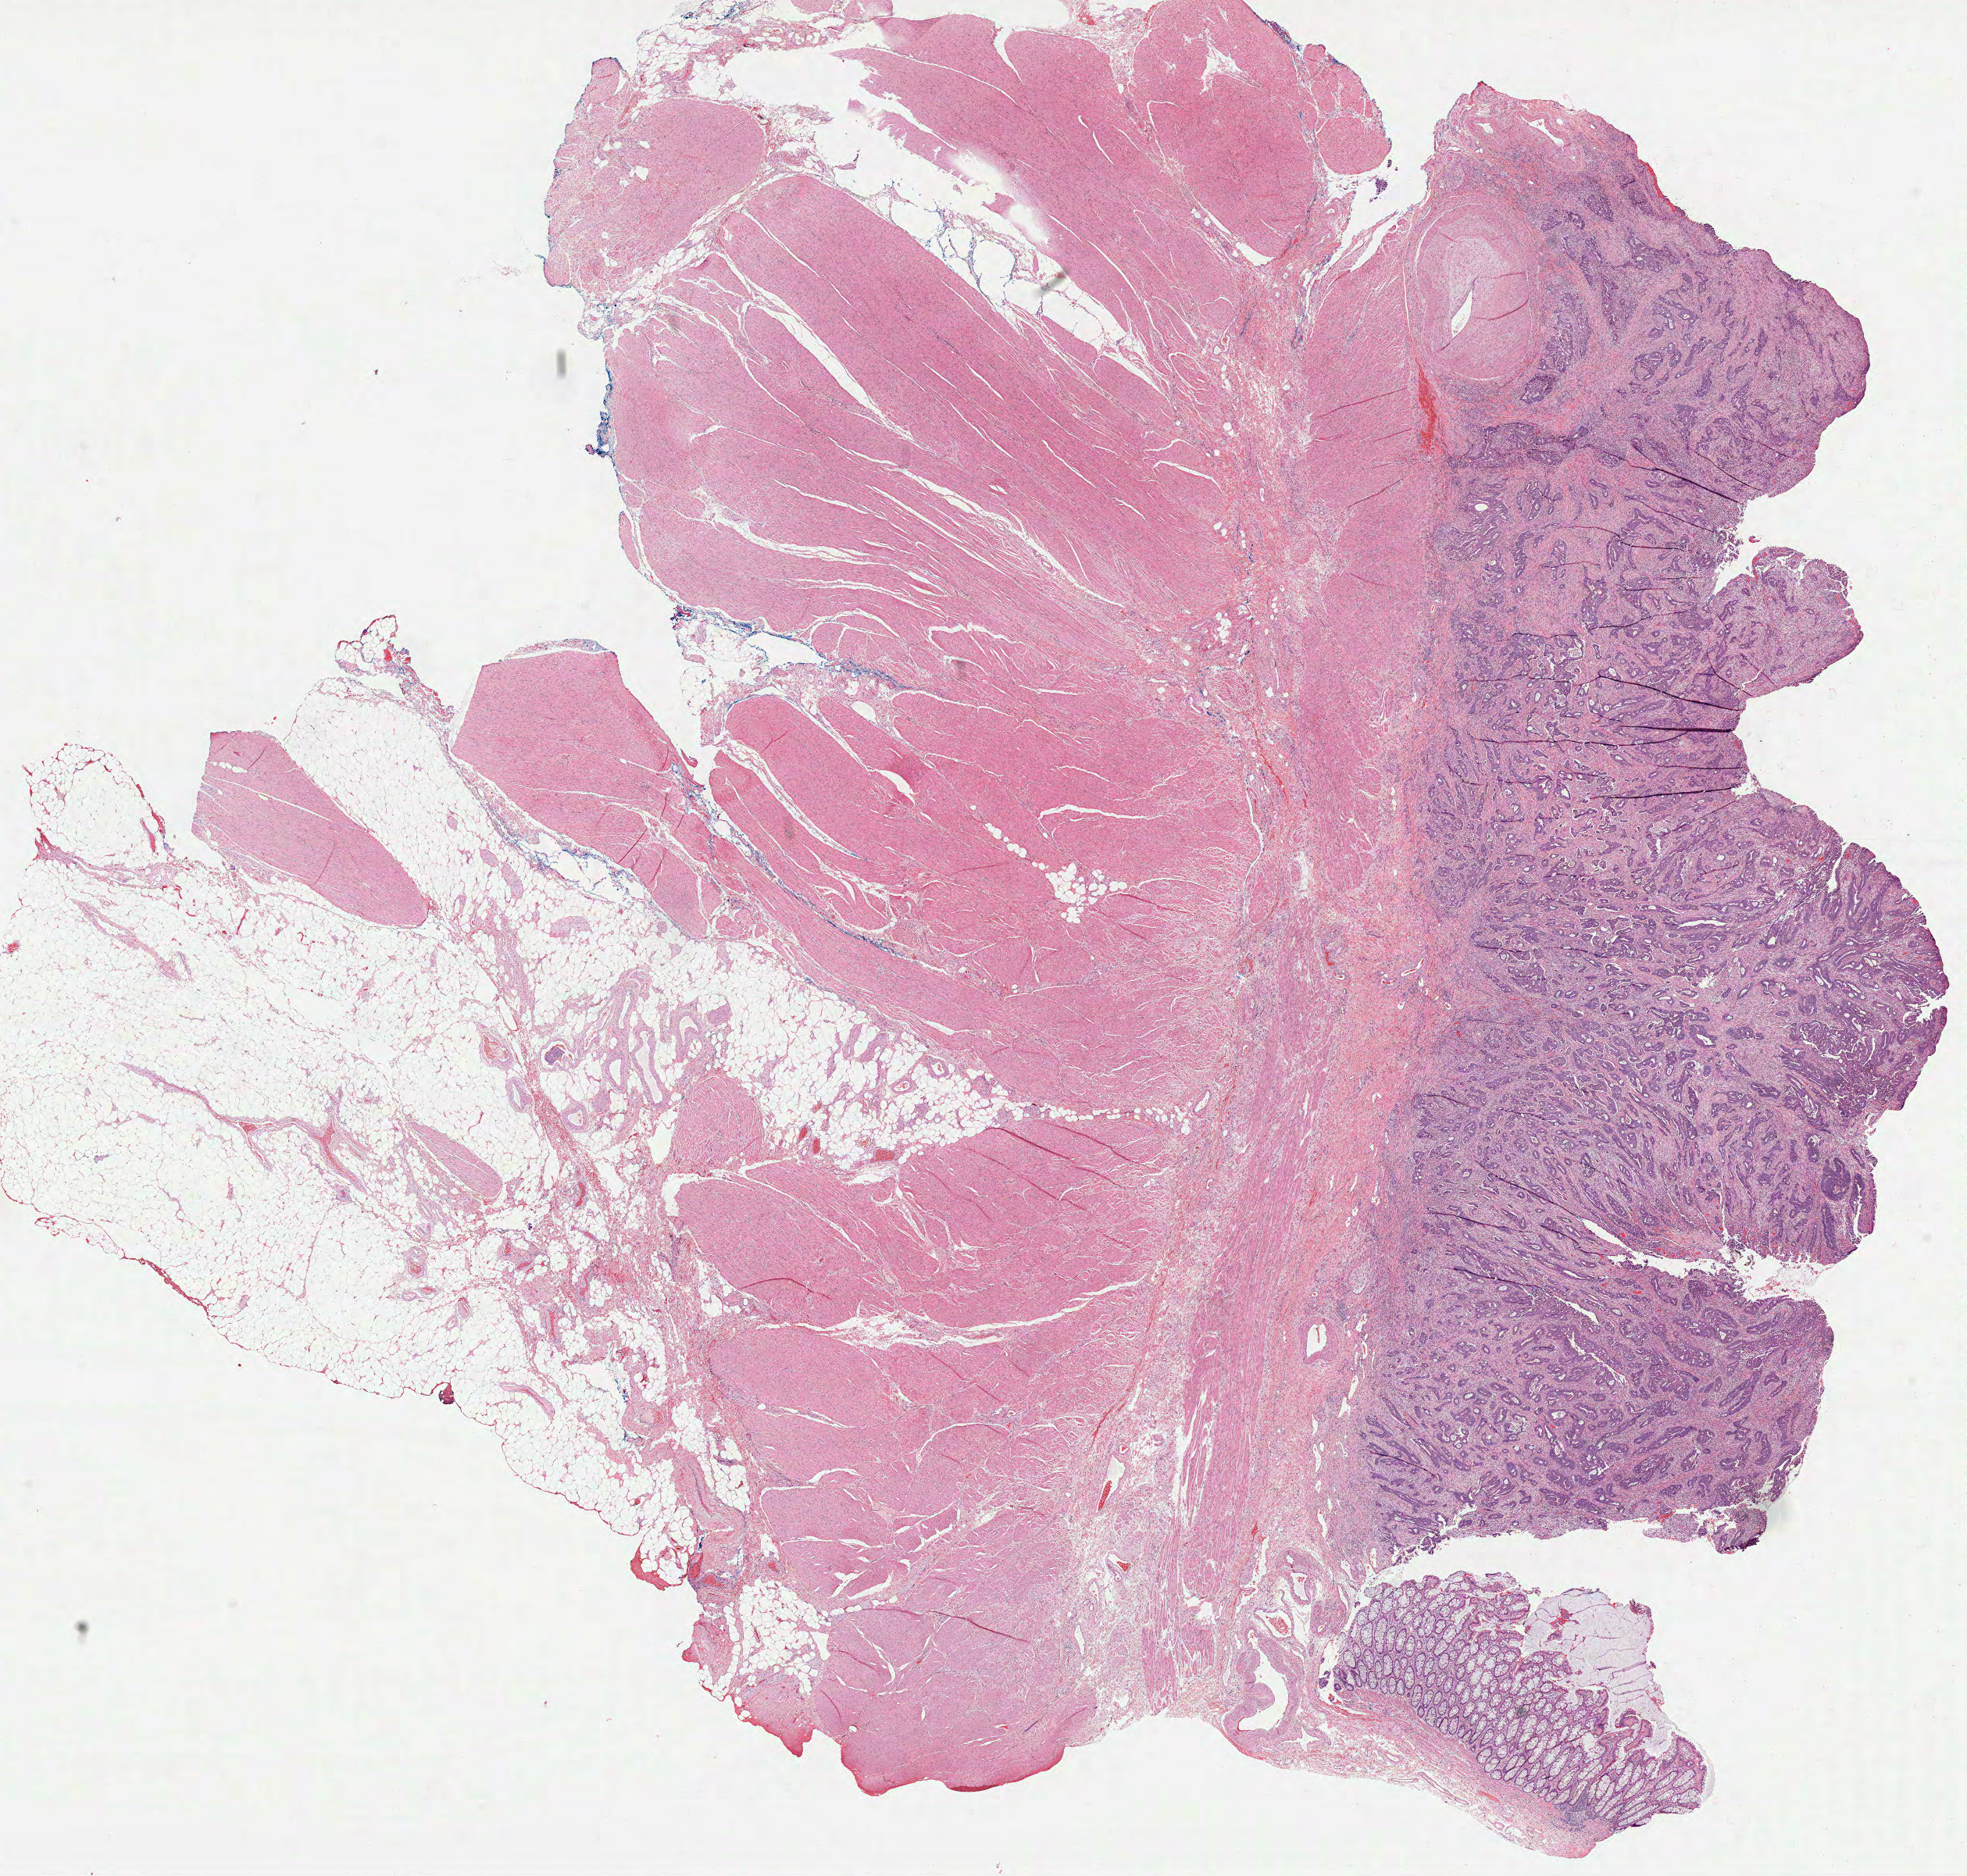
Digitized Hematoxylin and eosin (H&E) stained tissue section (whole slide) — shown as a low-resolution overview of the whole scanned area (about 20.3 x 19.4 mm); formalin-fixed paraffin-embedded (FFPE) diagnostic section; sample: primary tumour, colon. Male, age 69 years at initial diagnosis.
* TNM: T3 N1 M0
* lymph nodes positive (case pathology): 1 of 66 examined
* AJCC pathologic stage: IIIB (6th edition)
* diagnosis: Adenocarcinoma, NOS